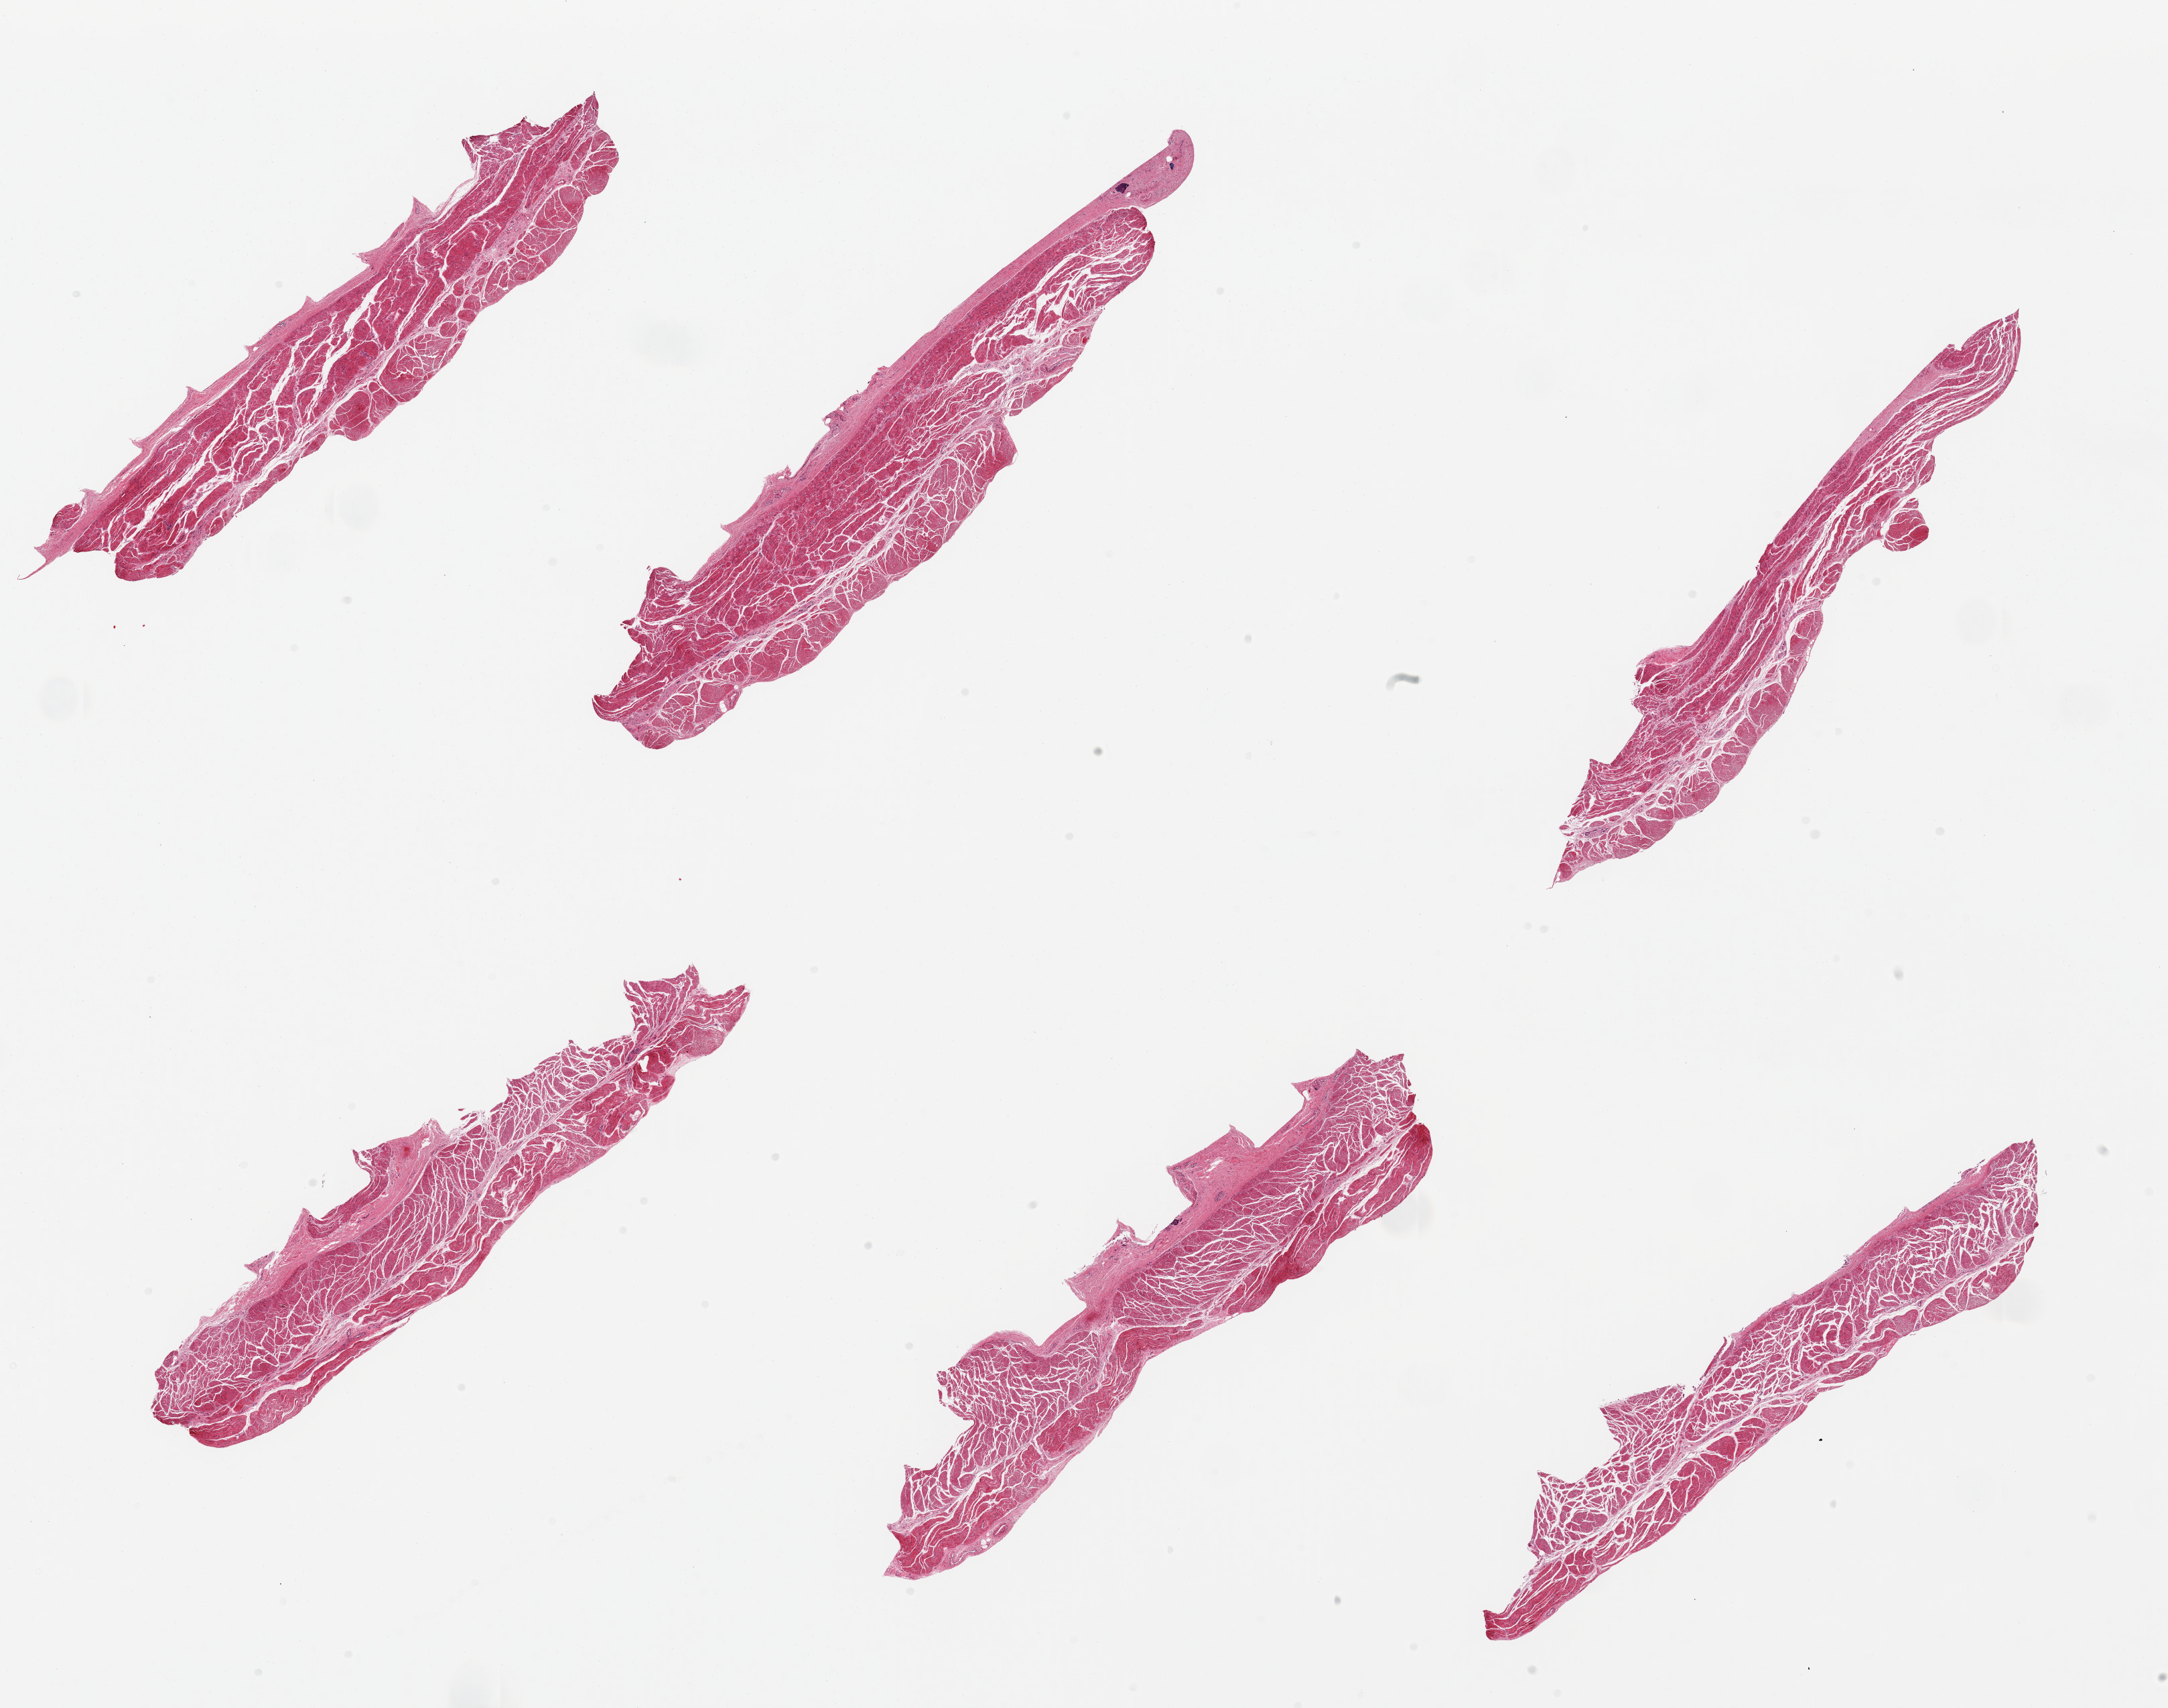
H&E whole-slide image, brightfield, shown as a low-resolution overview of the whole scanned area (about 25.6 x 20.2 mm, from a 20x scan), PAXgene-fixed paraffin-embedded (PFPE) section, section of esophageal muscle (target tissue), tissue donor sample. Donor sex: male.
• pathologist's review note for this sample: 6 pieces, all target muscularis